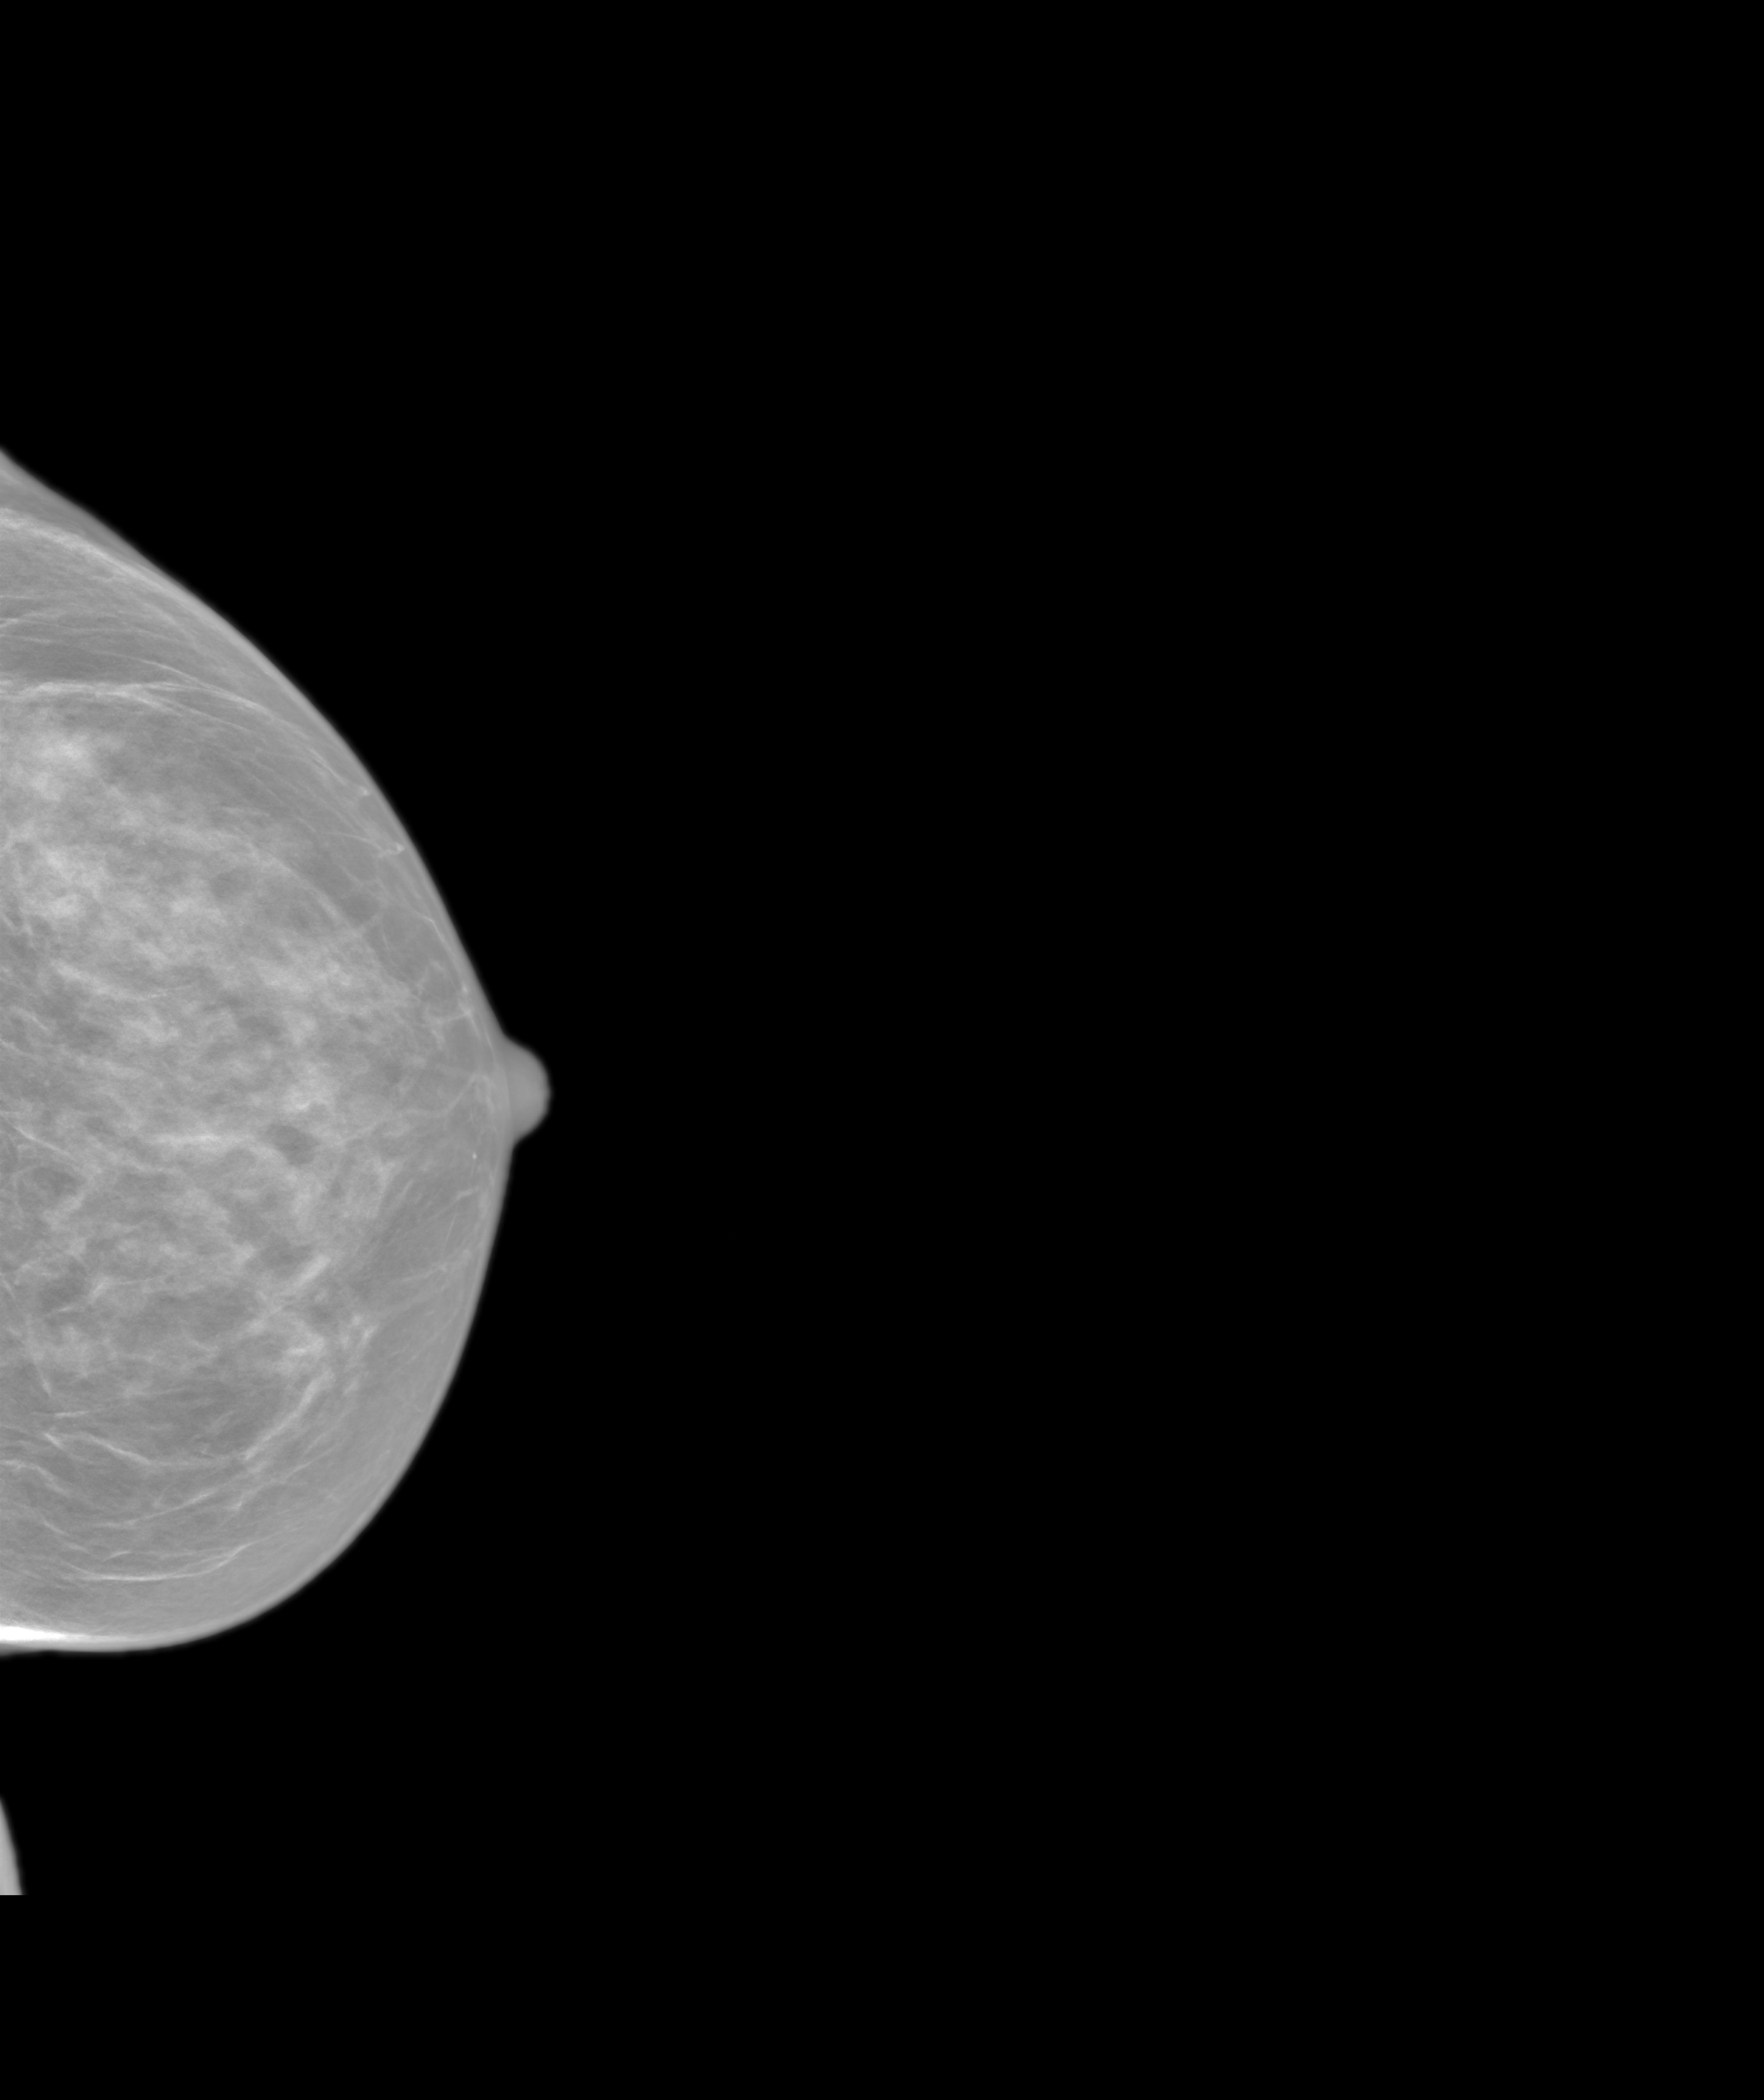
Screening examination. Female patient, age 57 years.
Image type: synthesized 2-D view from tomosynthesis. Breast: left. Projection: craniocaudal (CC) view.